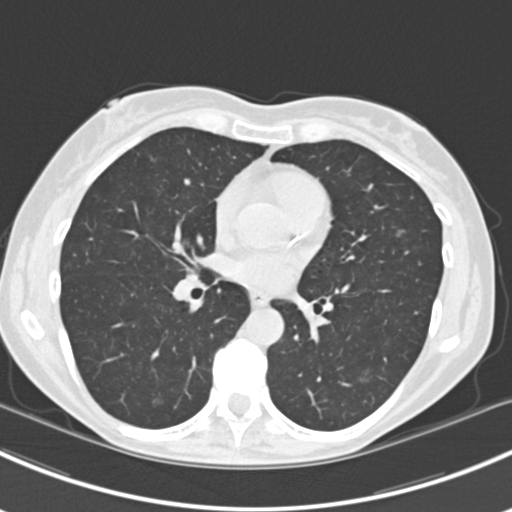
Chest CT (low-dose screening protocol), one axial image; first (baseline) screen; lung window (W 1500 / L -600 HU); 512 × 512 image matrix. Female, age 63 years at enrolment.
• Lesion marked by an expert reader, bounding box (x1, y1, x2, y2) in pixels: (378, 219, 423, 259).
• The screening reader recorded 10 non-calcified nodules or masses ≥4 mm on this exam (right lower lobe, right lower lobe, left lower lobe, left lower lobe, right middle lobe, right lower lobe, left lower lobe, left upper lobe, right upper lobe, left upper lobe); which of them this box marks is not recorded.
• Official screen result: positive, change unspecified: nodule(s) >= 4 mm or enlarging nodule(s), mass(es), or other non-specific abnormalities suspicious for lung cancer.
• Later outcome: lung cancer diagnosed 751 days after this screen — bronchiolo-alveolar adenocarcinoma, NOS, right upper lobe, right middle lobe, right lower lobe, left upper lobe, left lower lobe, moderately differentiated (G2), stage IV (AJCC 6th edition).